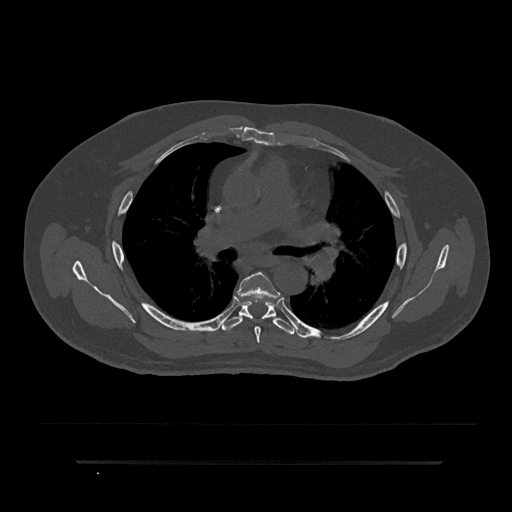
CT including the spine, one axial slice. Slice 551 of 797 in the series (ordered by position). Reconstruction kernel Br40s/3. Bone window (W 1800 / L 400 HU). 0.5 mm slice thickness. 512 × 512 image matrix, field of view 464 × 464 mm. Male patient, age 59 years. Case-level facts recorded for this patient, not image findings: primary cancer: bile ducts; vertebrae with lytic lesions (as recorded): T10.
Structures marked on this image (semi-automatic segmentation, software-assisted and operator-edited):
- T5 vertebra: bounding box <238,272,277,343> (left, top, right, bottom; pixels)
- T6 vertebra: <221,300,294,335>